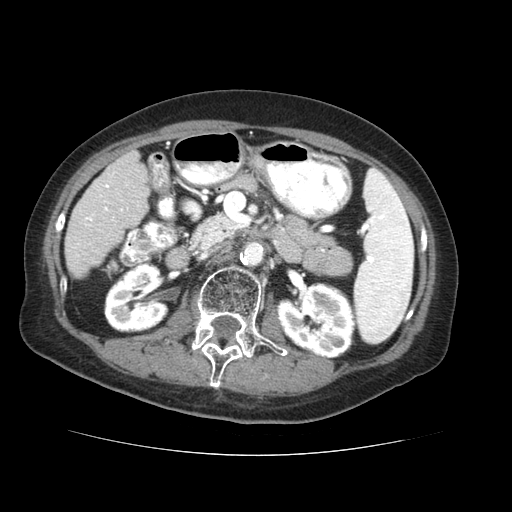
Contrast-enhanced abdominal CT (liver protocol), one axial slice; position 14 of 73 along the scan axis; 120 kVp; soft-tissue window (W 400 / L 40 HU); 2.5 mm slice thickness; 512 × 512 image matrix, field of view 360 × 360 mm. From the clinical record (not read from this slice): diagnosis: hepatocellular carcinoma (patient treated with transarterial chemoembolisation; whether this scan precedes or follows treatment is not stated here); TNM stage (as recorded): Stage-IVB; Child-Pugh class: A; tumour differentiation: well differentiated; tumour nodularity: uninodular.
Outlined on this slice (semi-automatic segmentation, software-assisted and operator-edited):
- liver parenchyma outside the tumour (the mass and vessels are separate outlines, so this box may not span the whole liver): bounding box [x1, y1, x2, y2] px = [64, 150, 148, 278]
- liver vessels: [77, 172, 123, 257]